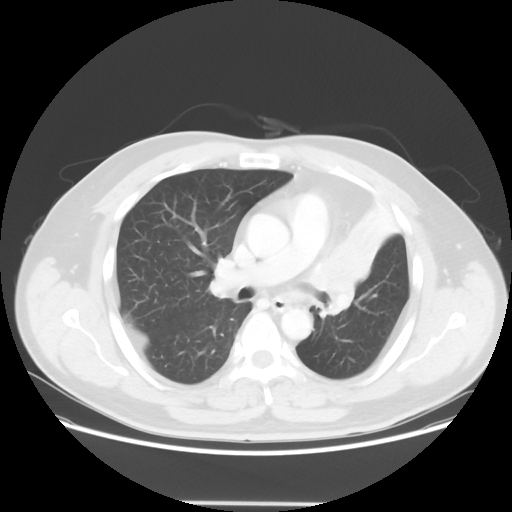
Chest CT, one axial slice; position 37 of 62 along the scan axis; reconstruction kernel STANDARD; lung window (W 1500 / L -600 HU); 512 × 512 image matrix, field of view 403 × 403 mm. Patient: male, 49 years. From the clinical record (not read from this slice): clinical TNM (as recorded): T3 N3 M1c.
Structures marked on this image (bounding box drawn by a radiologist):
- lung tumour (recorded histology: squamous cell carcinoma): box from (x=309, y=224) to (x=381, y=312) px